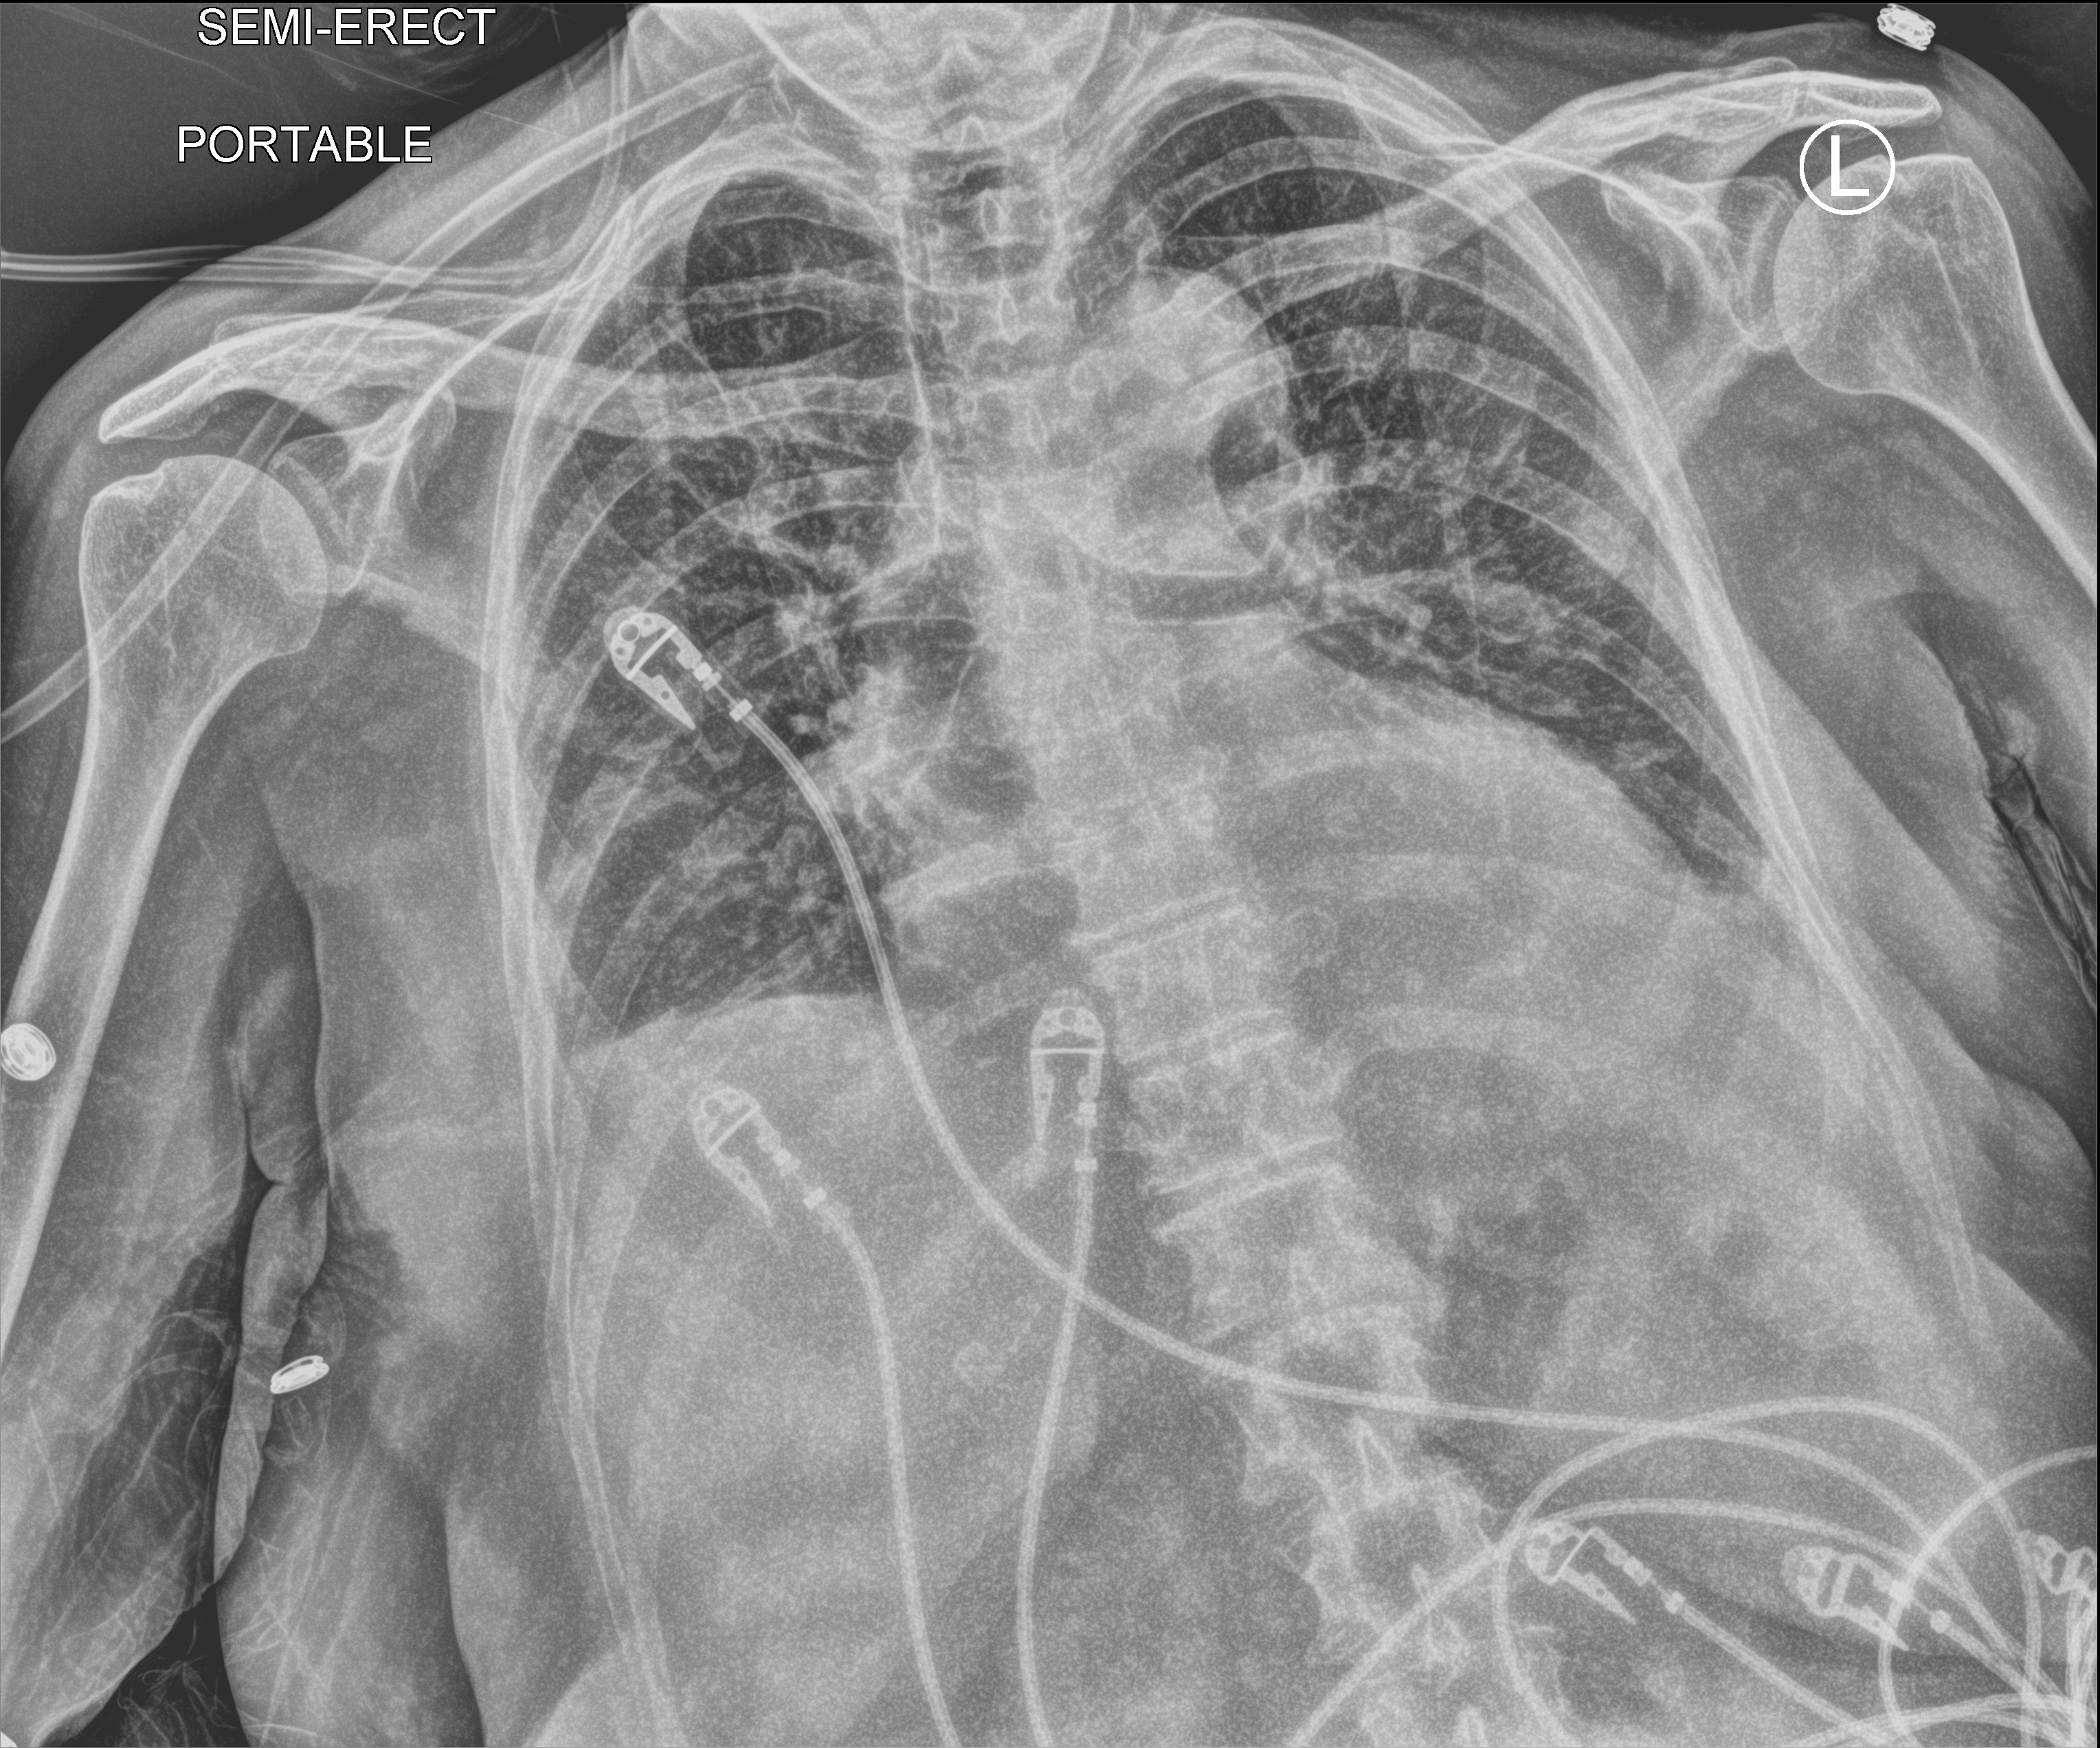
Portable chest radiograph, anteroposterior (AP) projection. Female patient hospitalised with COVID-19, age 75–90 years.
From the hospital-stay record, not from the radiograph (when in the stay this image was taken is not recorded):
- admitted to intensive care during this hospital stay: no
- mechanically ventilated during this hospital stay: no